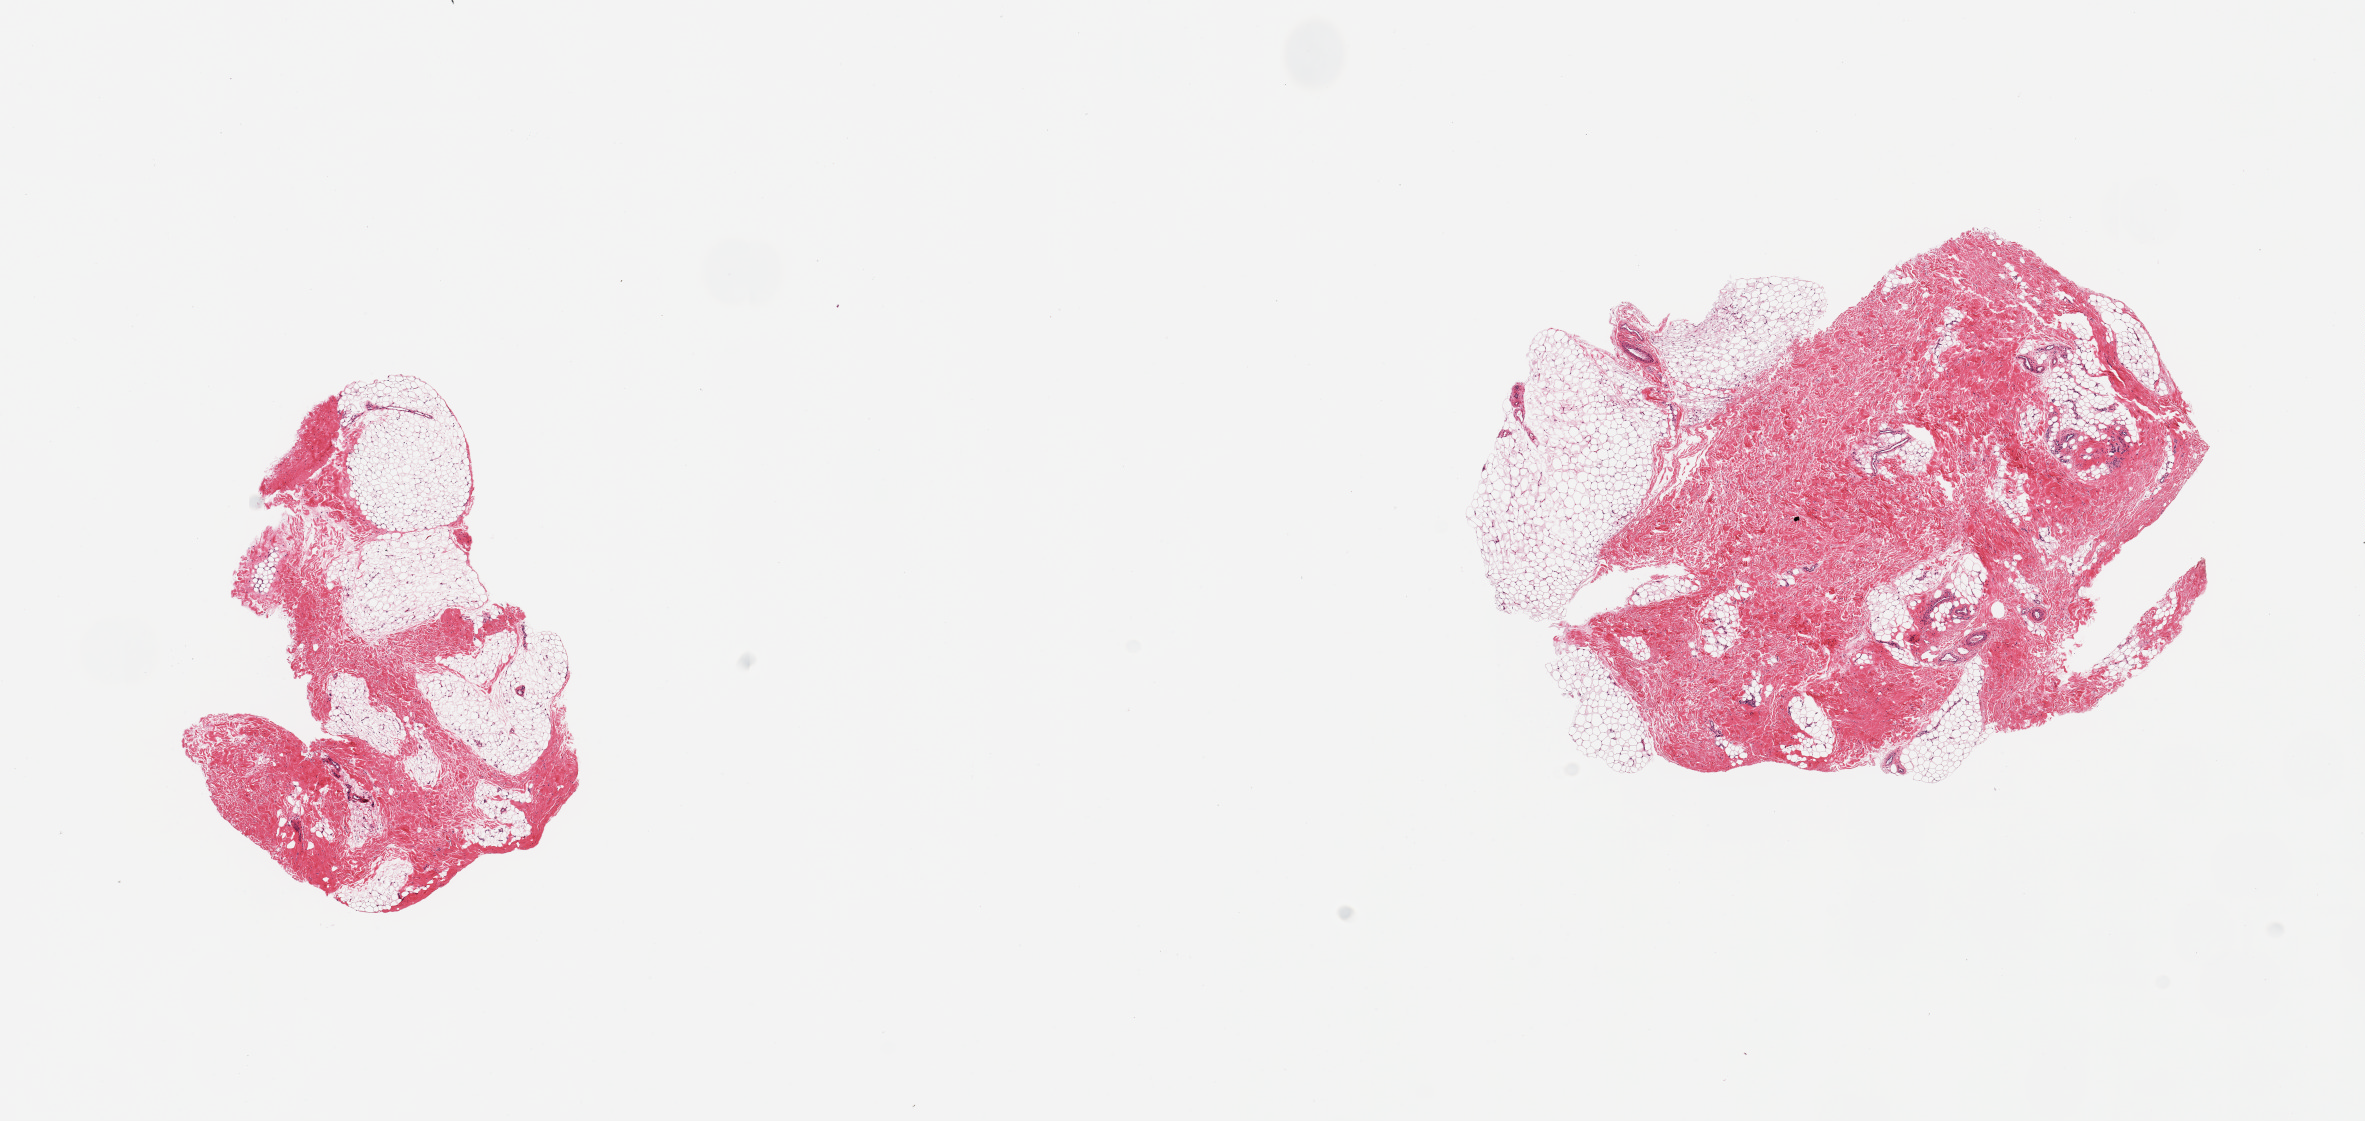
Haematoxylin and eosin whole-slide image, brightfield — a low-resolution overview of the entire scanned area, about 18.7 x 8.9 mm (from a 20x scan); PAXgene-fixed, paraffin-embedded tissue; section of breast (target tissue); donor tissue sample. Donor sex: male.
Pathologist's review note for this sample: 2 pieces; fibrofatty tissue without ducts.